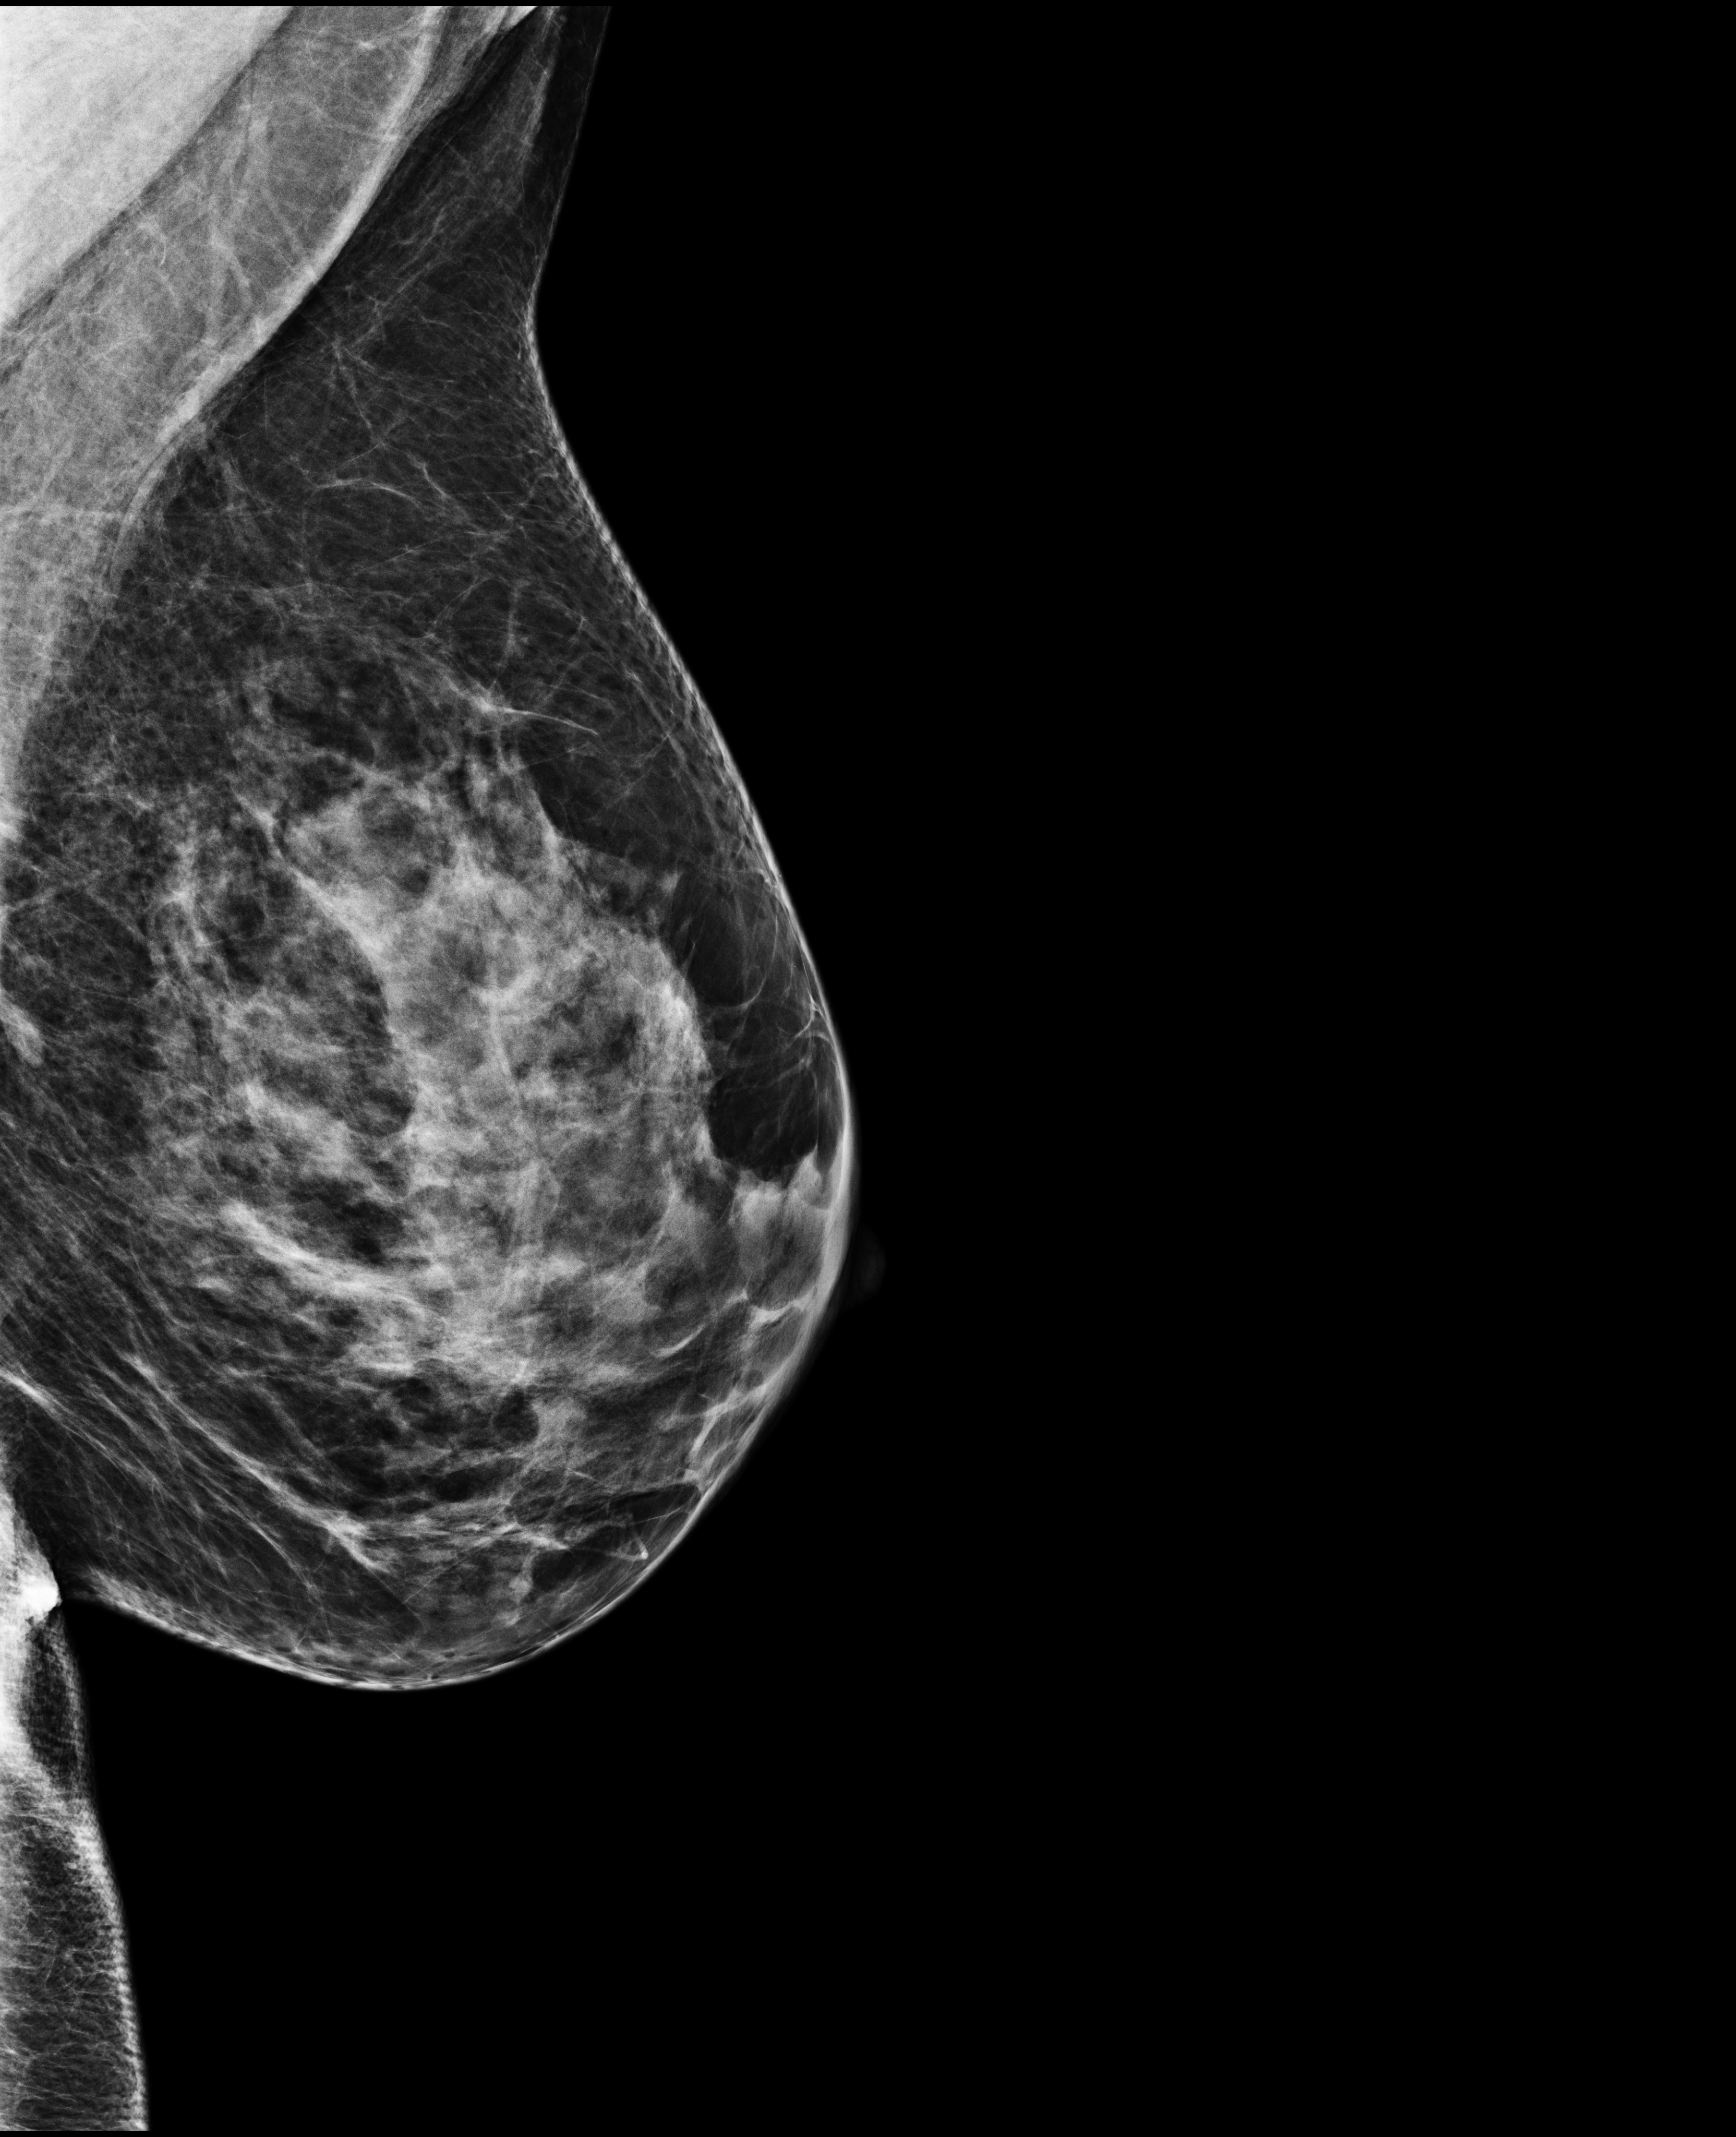
Screening examination.
Image type: full-field digital mammogram. Breast: left. Projection: mediolateral oblique (MLO) view.